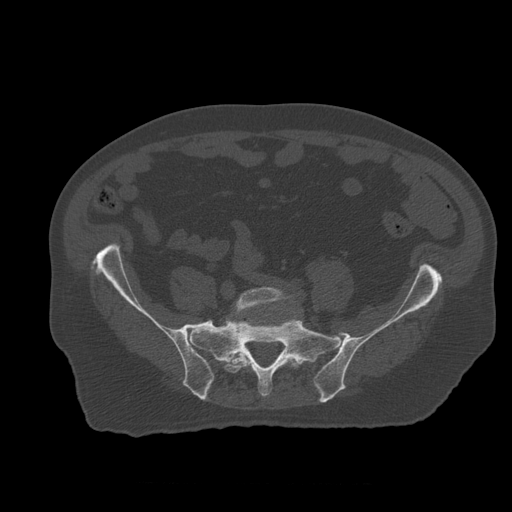
CT including the spine, one axial slice; position 127 of 399 along the scan axis; 120 kVp; bone window (W 1800 / L 400 HU); 1.25 mm slice thickness; 512 × 512 image matrix, field of view 407 × 407 mm. Patient age 73 years. Case-level facts recorded for this patient, not image findings: primary cancer: prostate; vertebrae with lytic lesions (as recorded): L2.
Annotated regions visible in this slice (semi-automatically segmented with operator editing):
- L5 vertebra: bounding box [x1, y1, x2, y2] px = [224, 287, 301, 374]